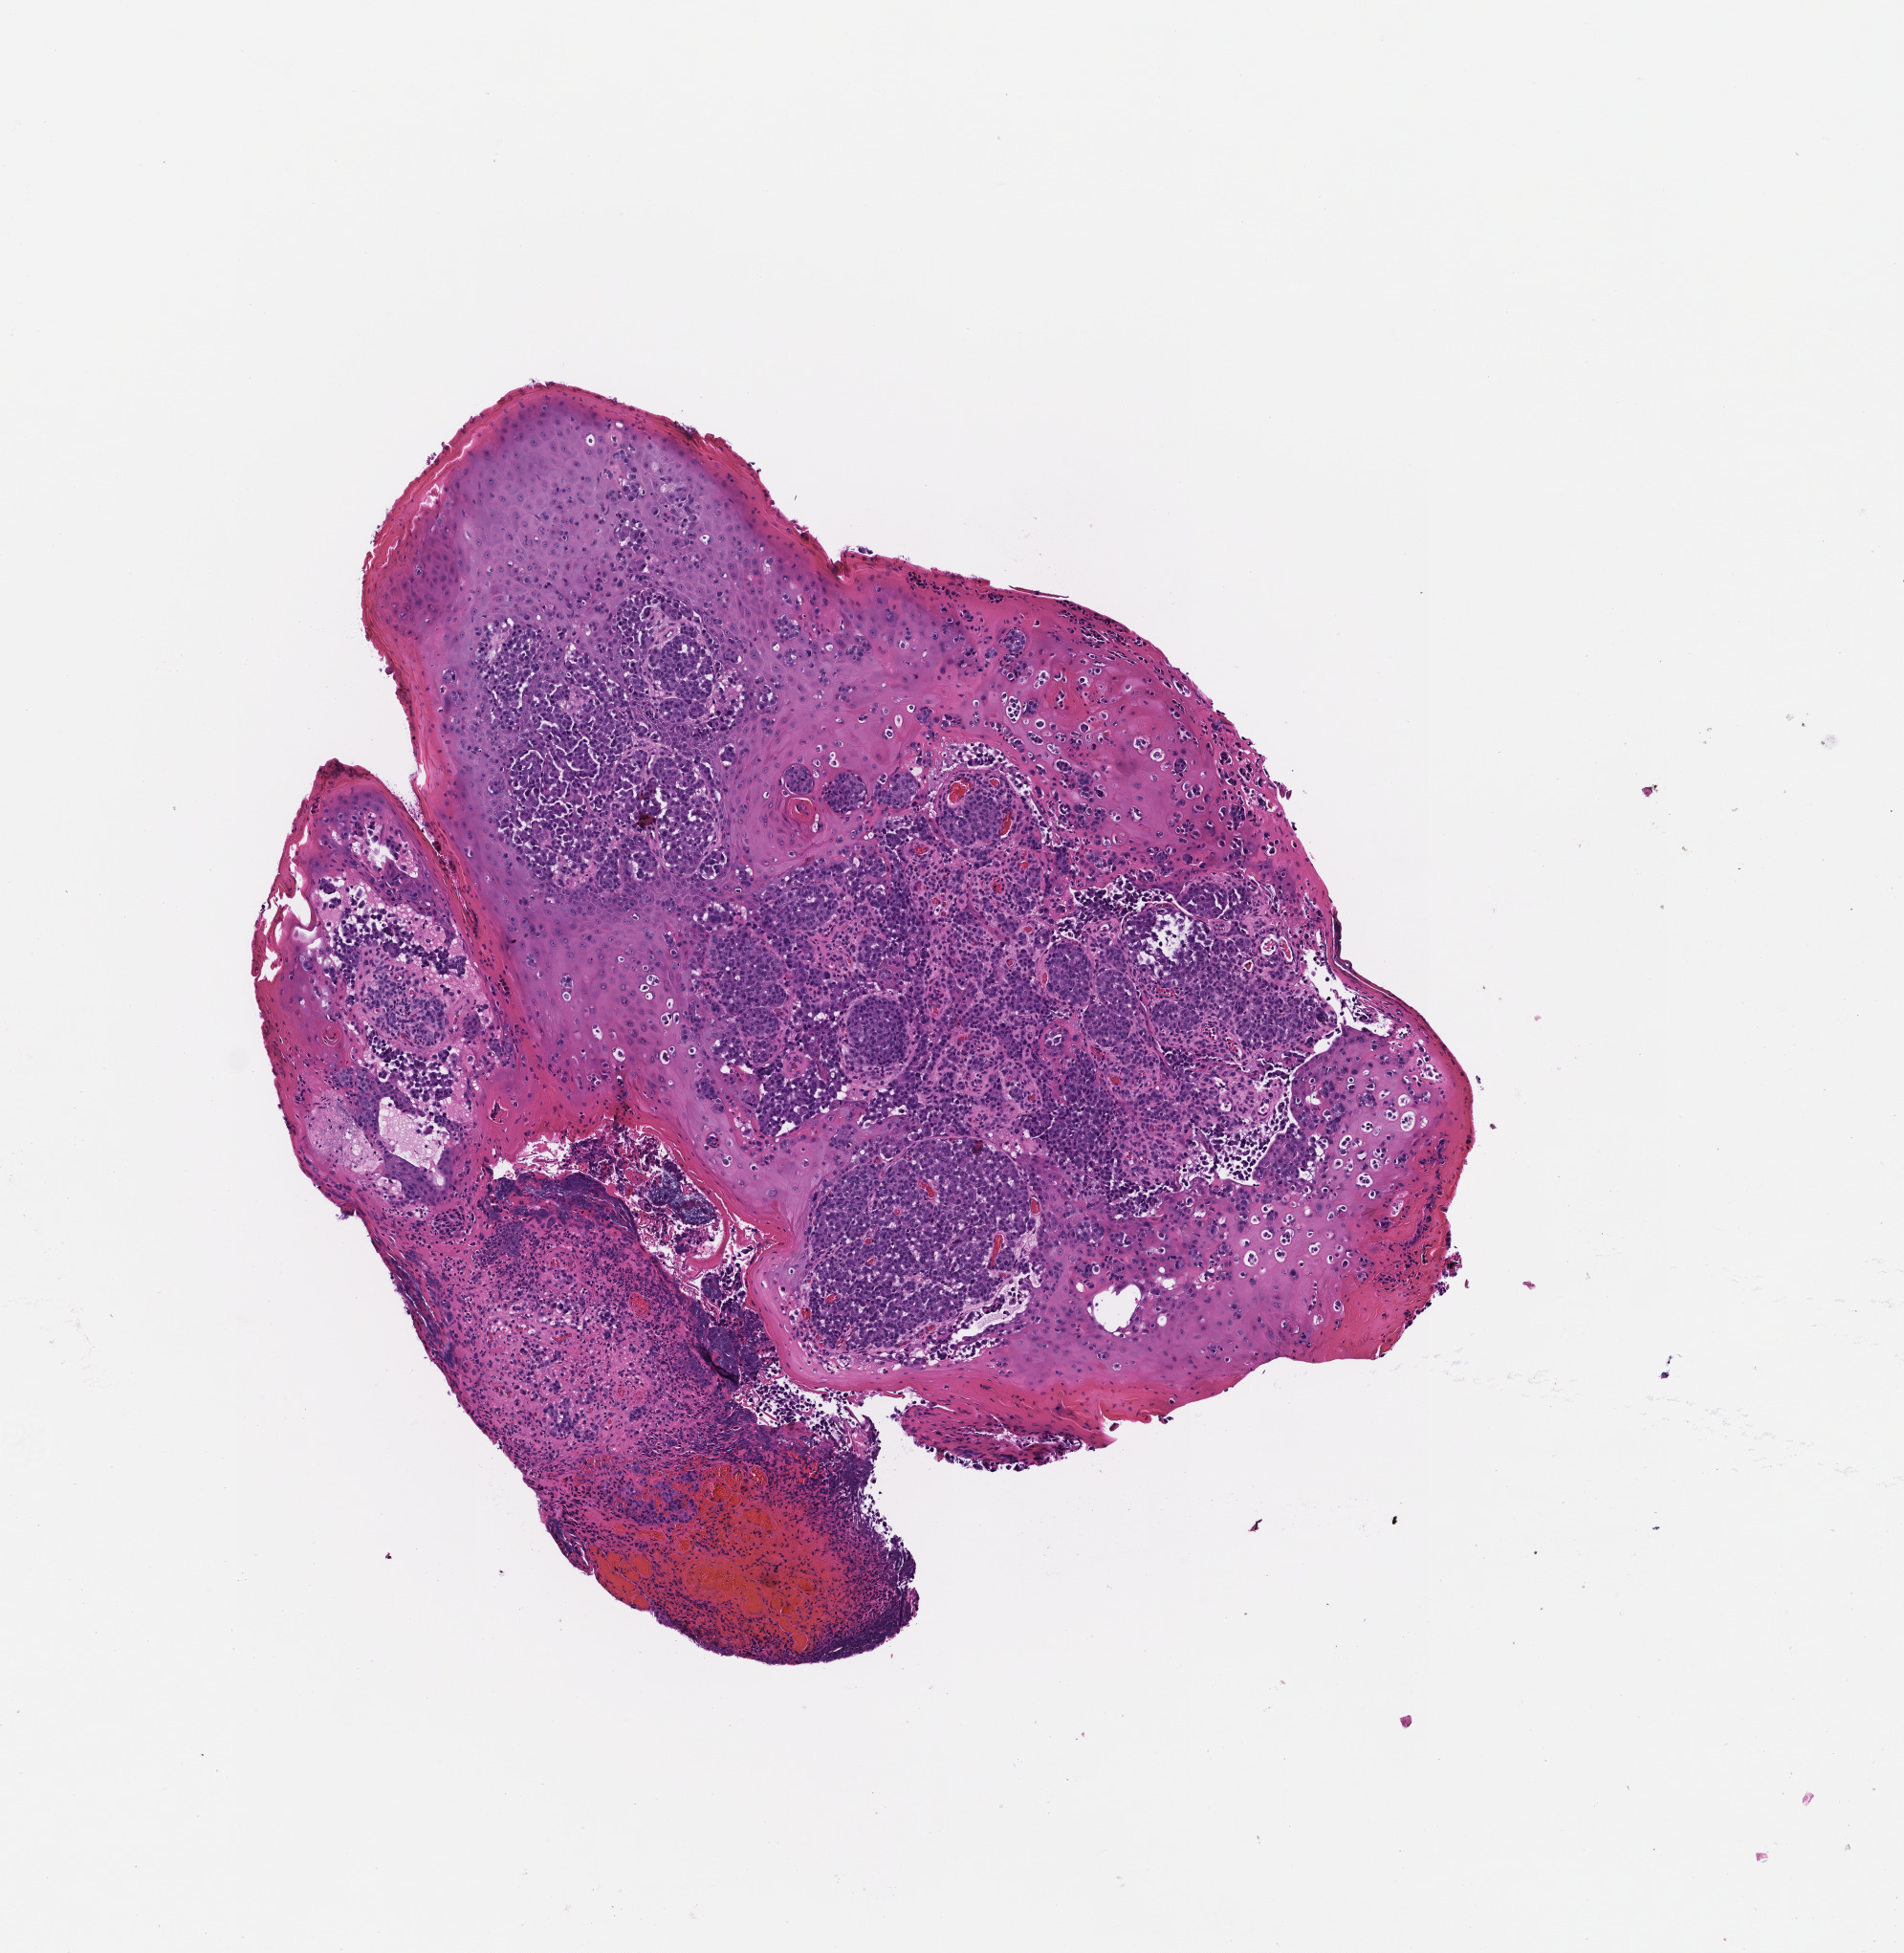
Hematoxylin and eosin (H&E) whole-slide image, a low-resolution overview of the entire scanned area, about 4.0 x 4.1 mm, formalin-fixed, paraffin-embedded (FFPE) tissue, site: skin, specimen time point: collected at baseline (before treatment). Male patient.
• this section: primary tumor
• diagnosis: Melanoma